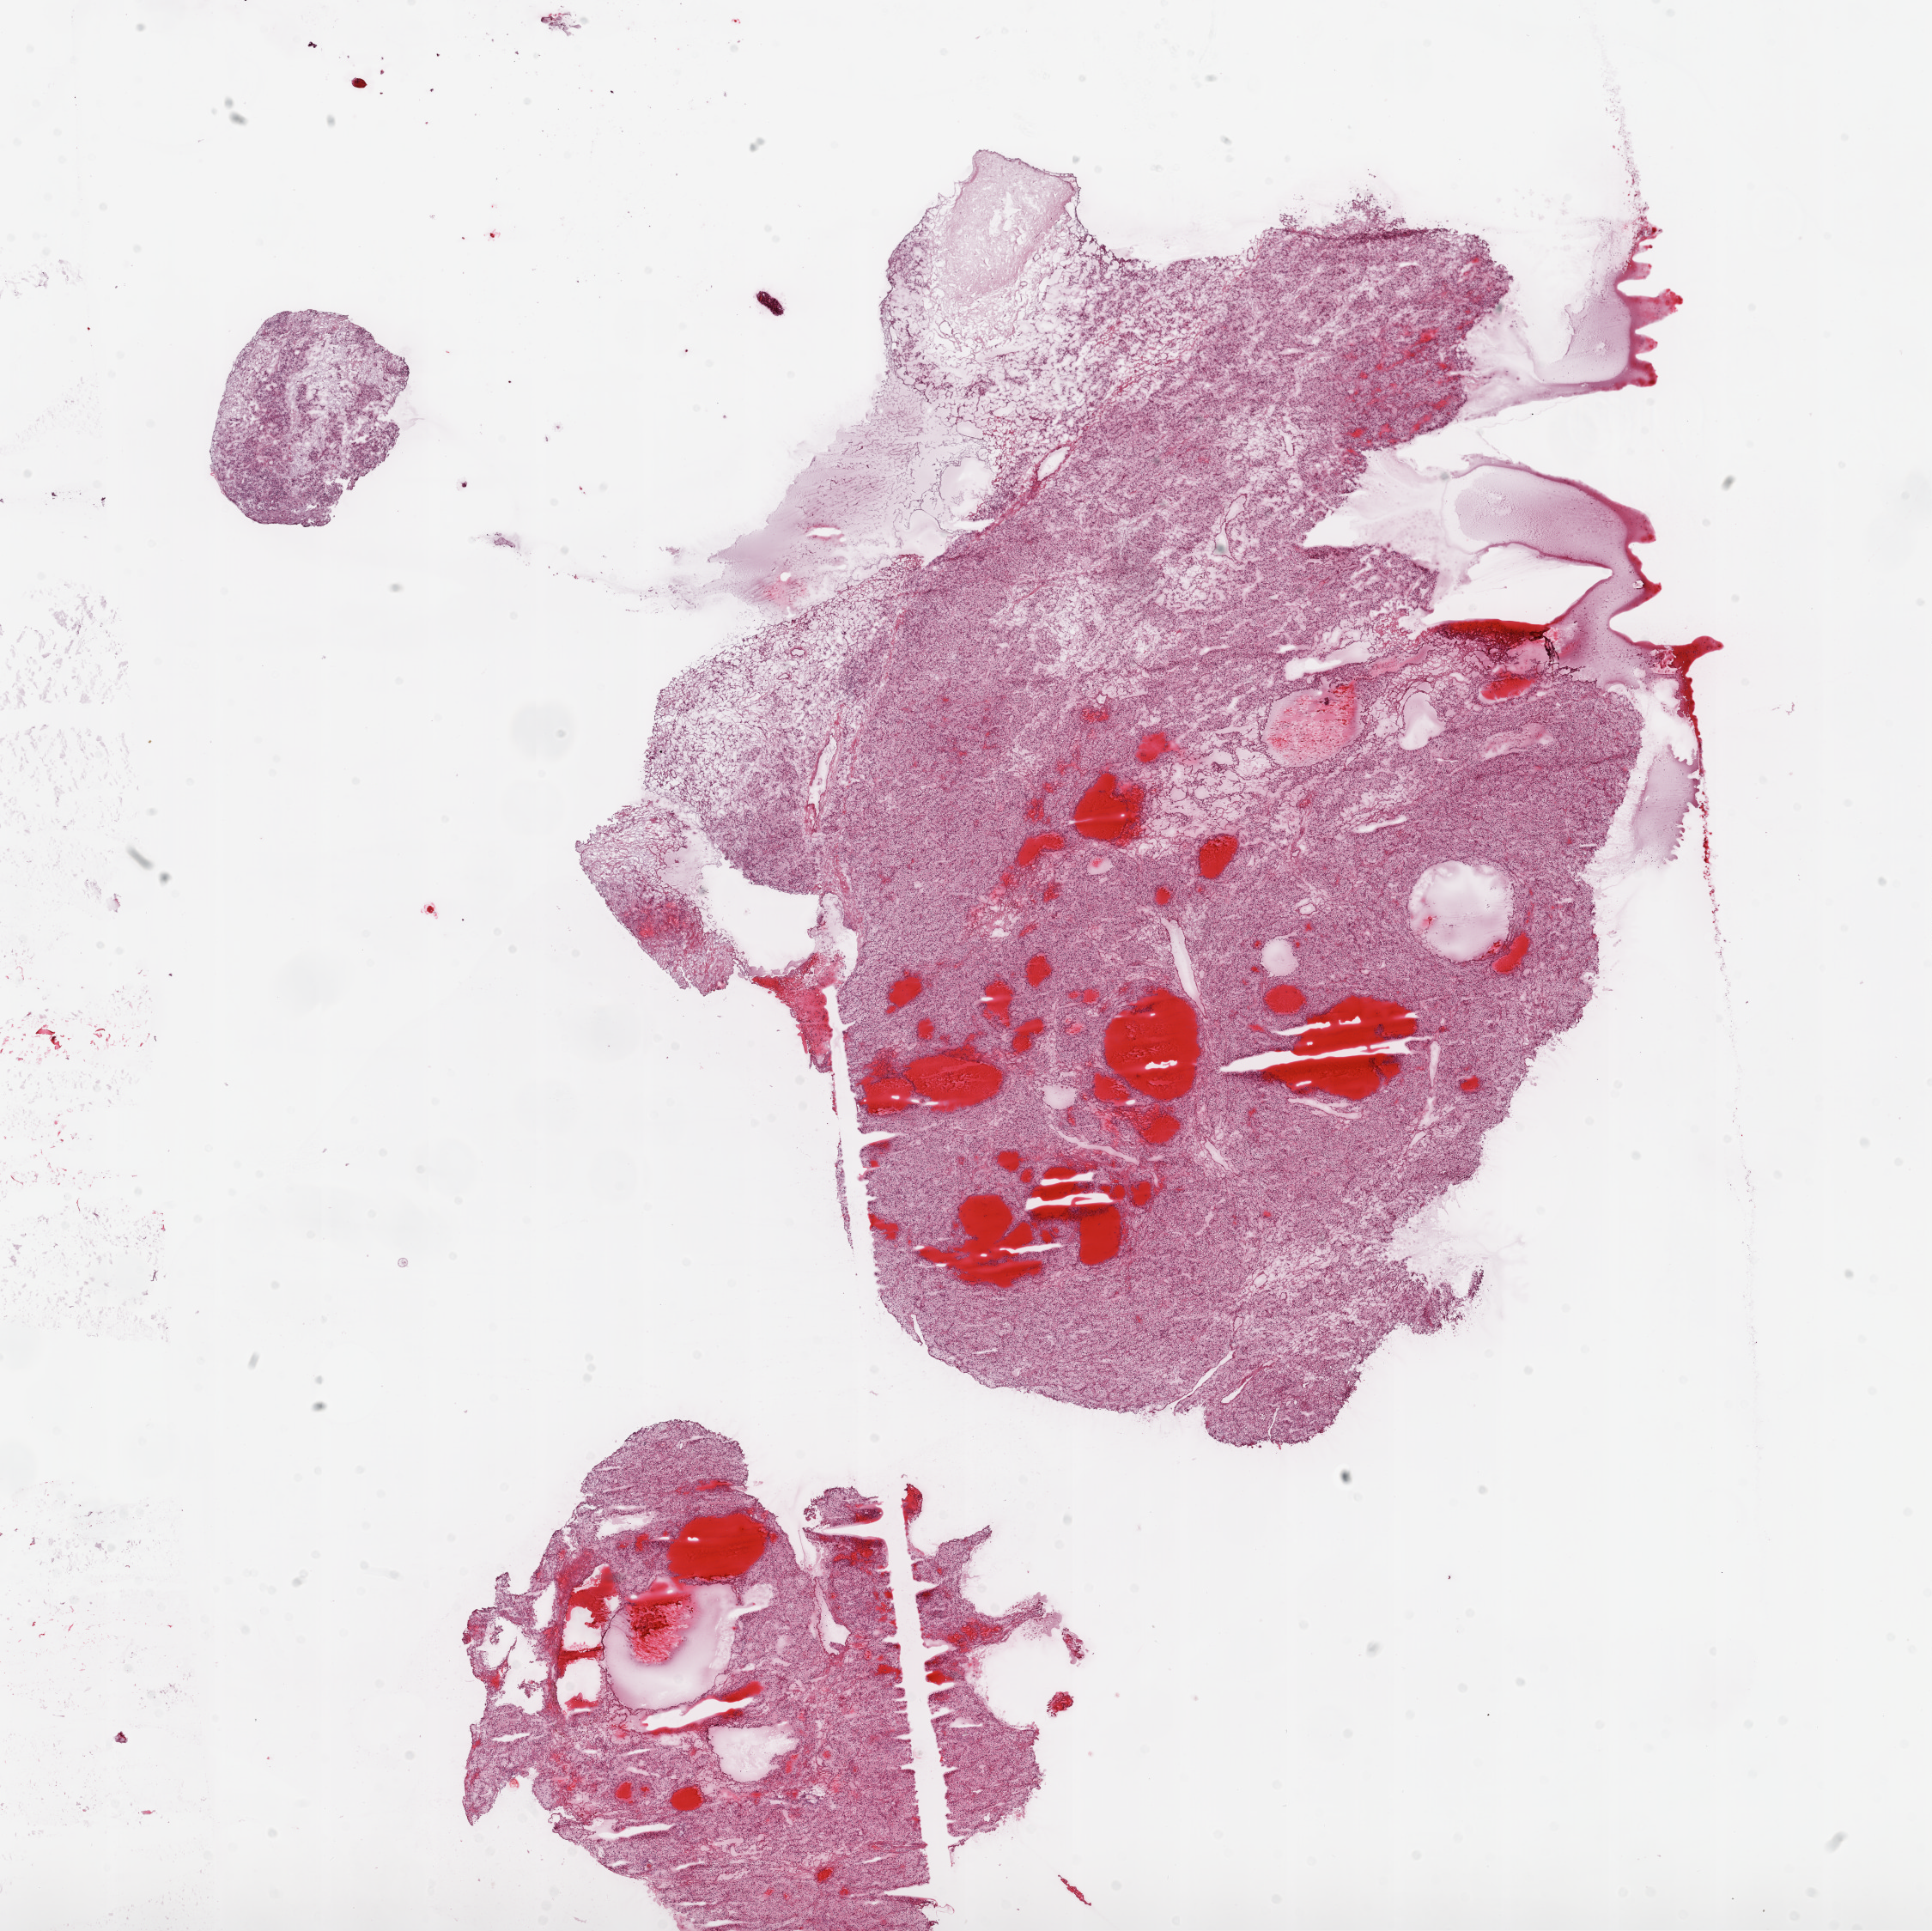
Digitized H&E-stained tissue section (whole slide), shown as a low-resolution overview of the whole scanned area (about 18.1 x 18.0 mm, acquisition: 20x scan); frozen section; primary tumour sample from the kidney. Female patient; age at initial diagnosis 41 years. Histologic grade: G2 (moderately differentiated). Composition of this section per pathologist review: tumour cells 85%, tumour nuclei 85%, normal cells 0%, stromal cells 15%, necrosis 0%.
* AJCC pathologic stage: I
* laterality: left
* histologic diagnosis: Clear cell adenocarcinoma, NOS